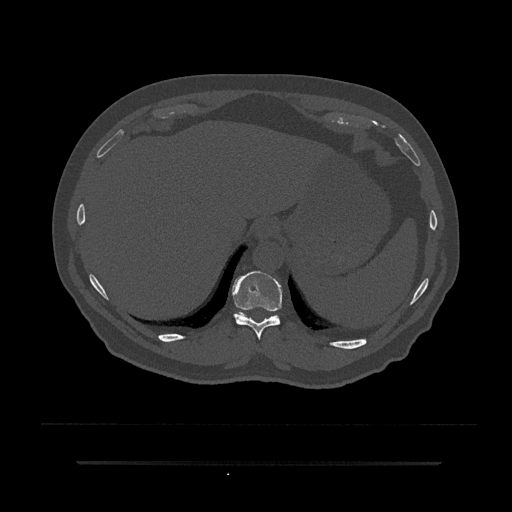
CT including the spine, one axial slice; position 317 of 797 along the scan axis; reconstruction kernel Br40s/3; 120 kVp; bone window (W 1800 / L 400 HU); 0.5 mm slice thickness; 512 × 512 image matrix. Patient: male, 59 years. Case-level facts recorded for this patient, not image findings: primary cancer: bile ducts; vertebrae with lytic lesions (as recorded): T10.
Annotated regions visible in this slice (semi-automatically segmented with operator editing):
- T10 vertebra: bounding box <232,271,282,339> (left, top, right, bottom; pixels)
- T11 vertebra: <236,313,276,319>